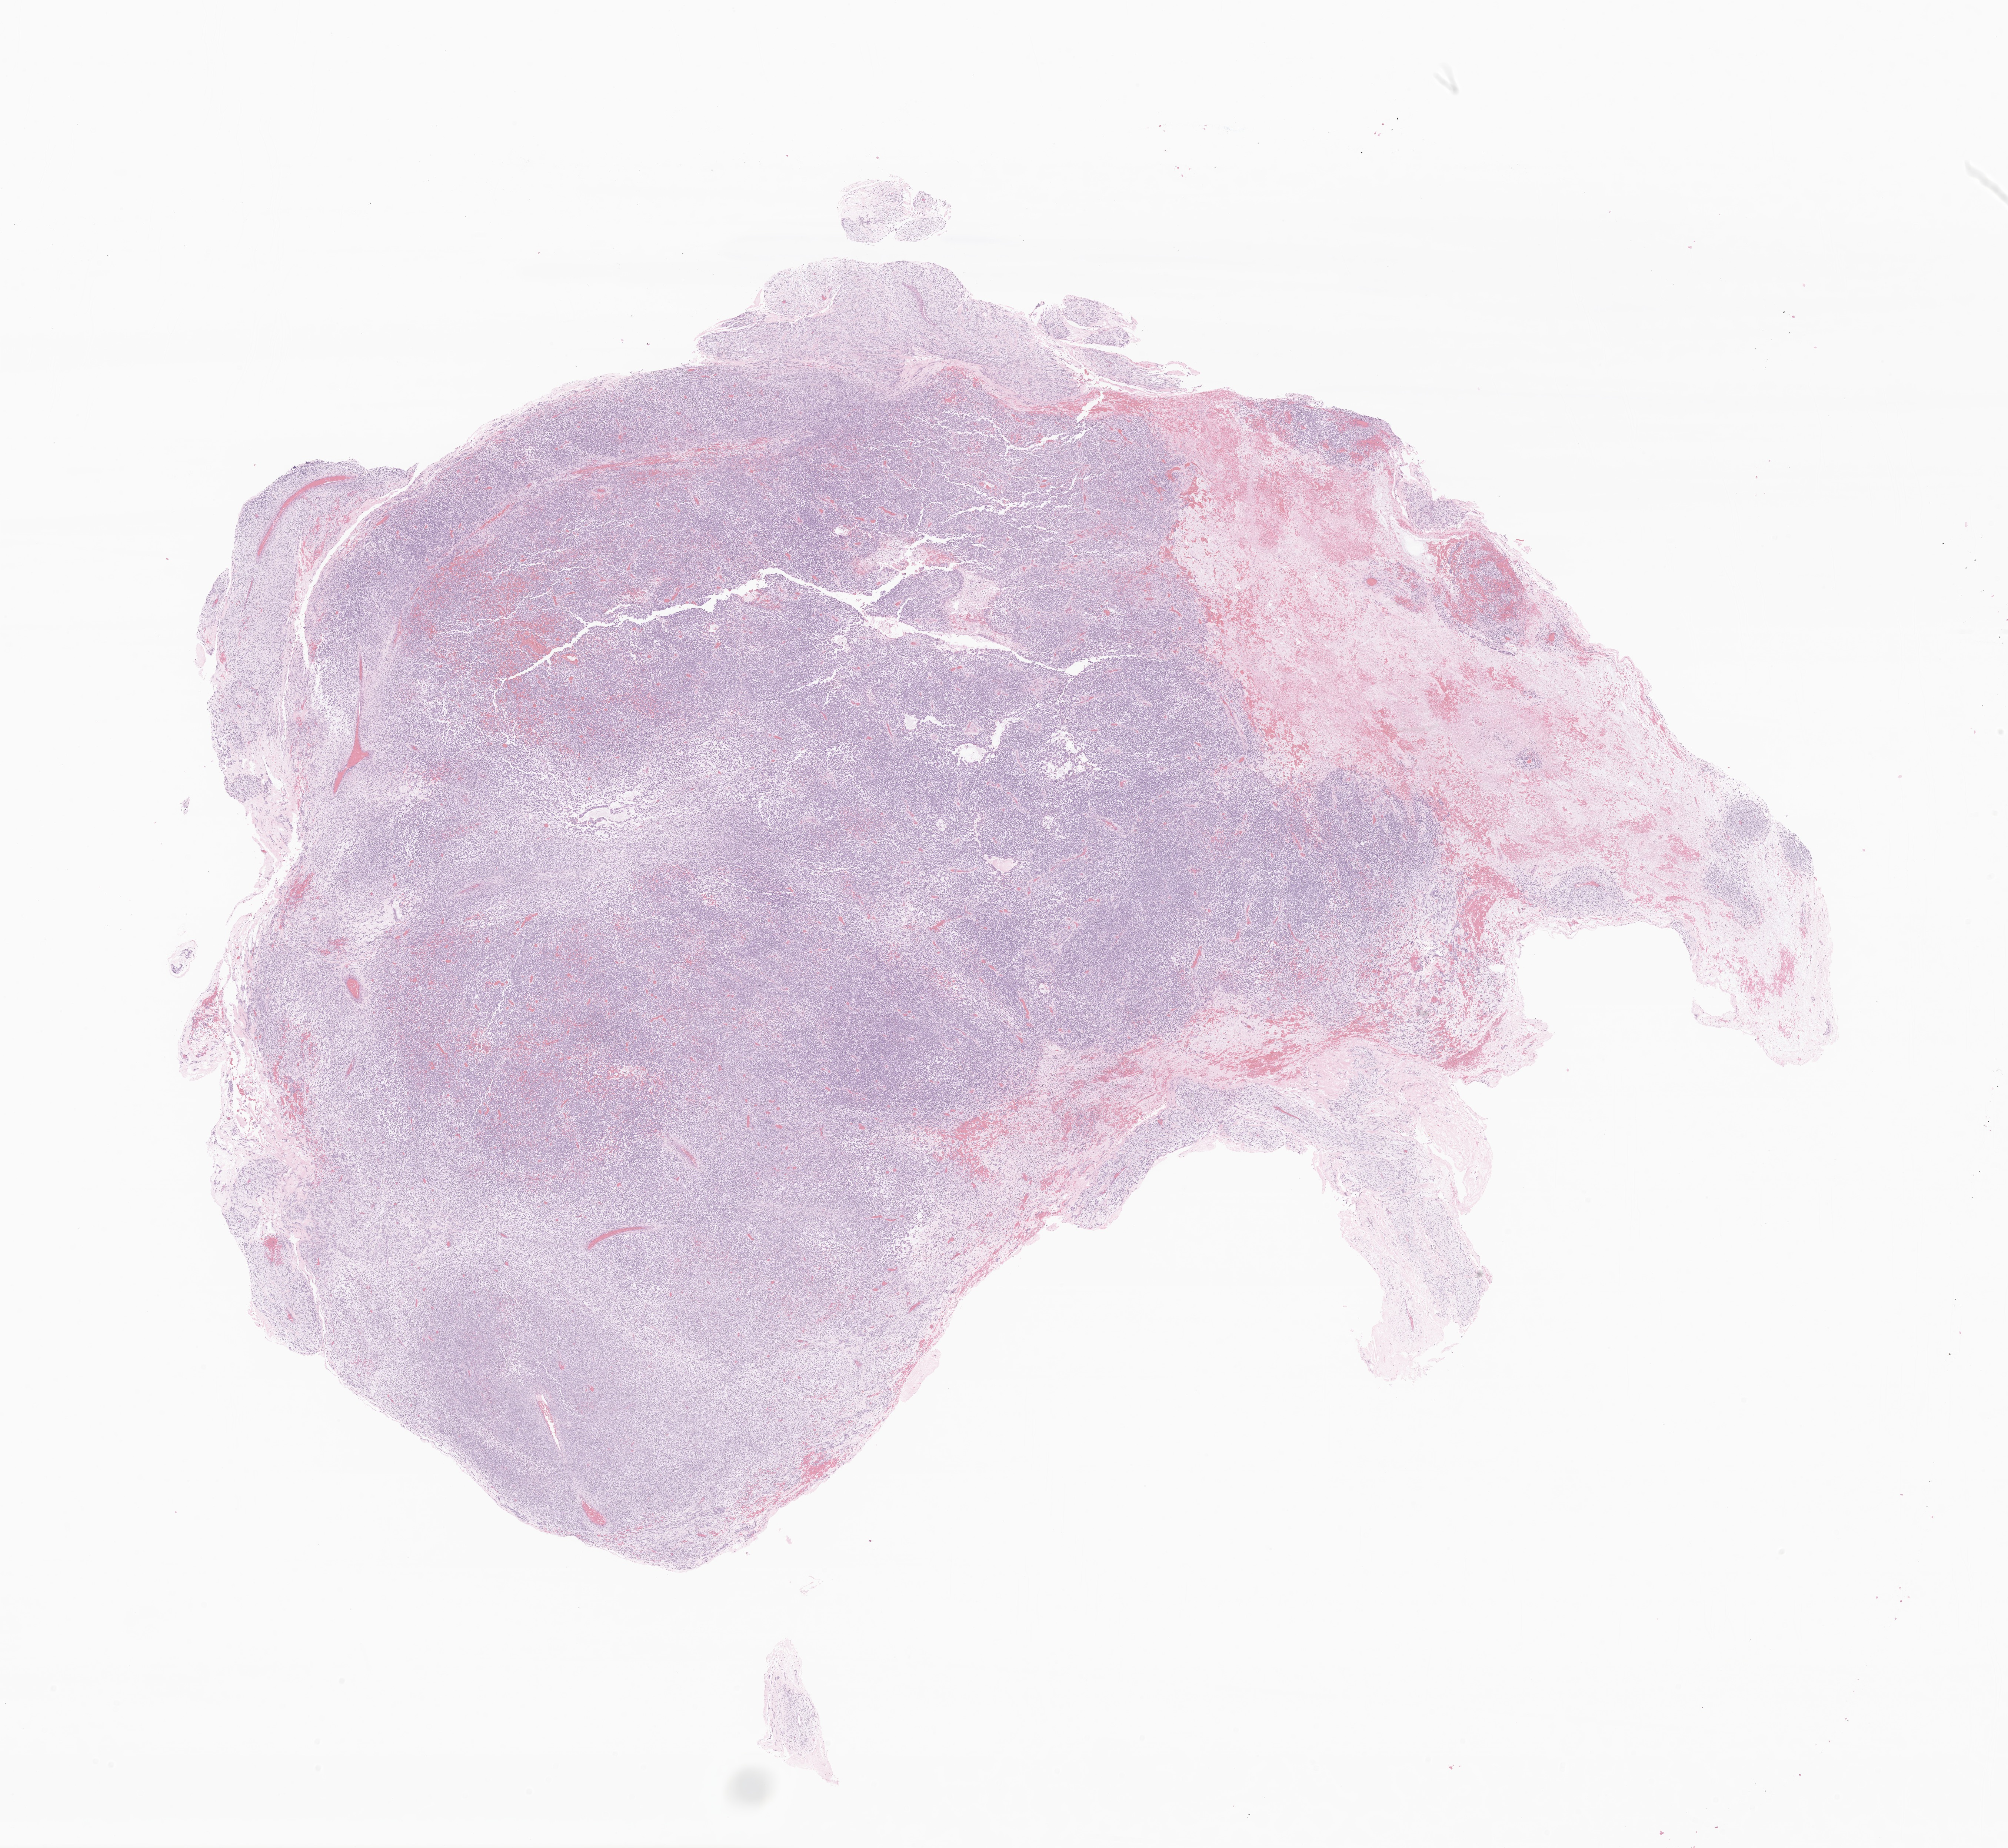
Digitized H&E-stained section of tumor tissue from the male genital organ, a low-resolution overview of the entire scanned area, about 22.9 x 21.0 mm, FFPE section. Male patient, age 207 months (17 years 3 months).
Diagnosis: Small cell sarcoma.